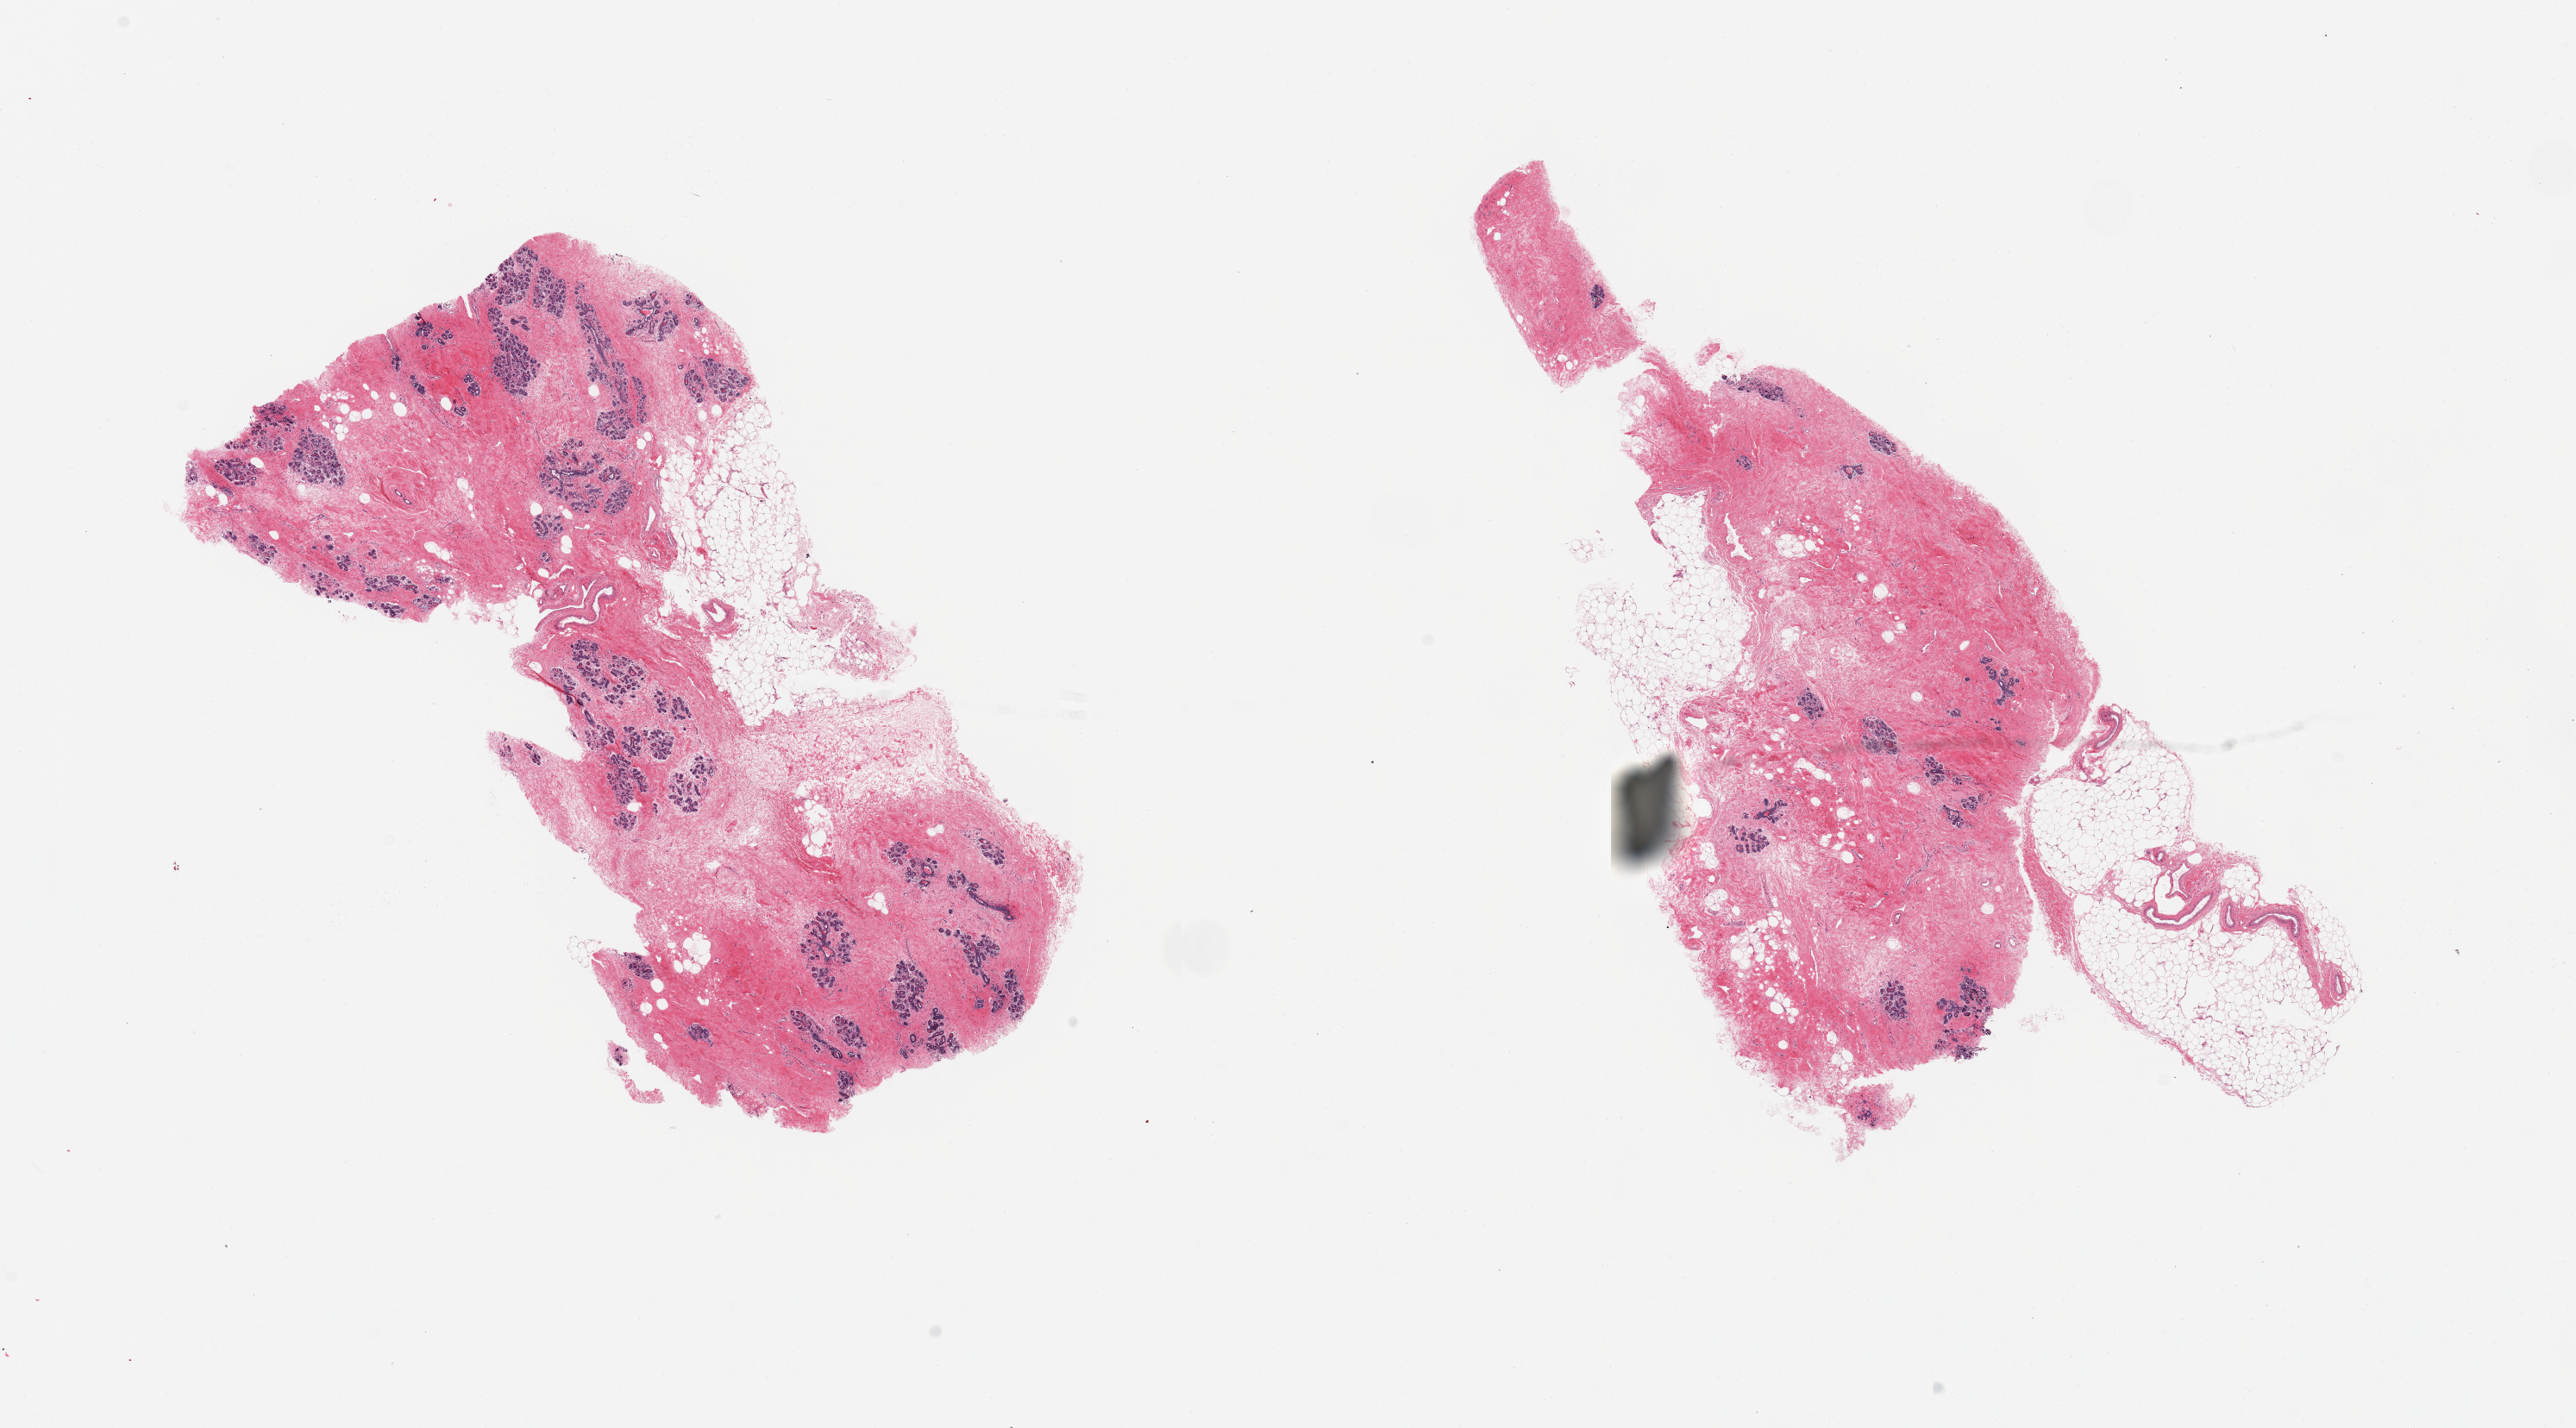
H&E whole-slide image — shown as a low-resolution overview of the whole scanned area (about 23.6 x 13.1 mm, acquisition: 20x scan), PAXgene-fixed paraffin-embedded (PFPE) section, section of breast (target tissue), tissue donor sample. Donor: female.
Reviewer comment on this tissue sample: 2 pieces, non-neoplastic breast tissue with no greater than 20% fat.